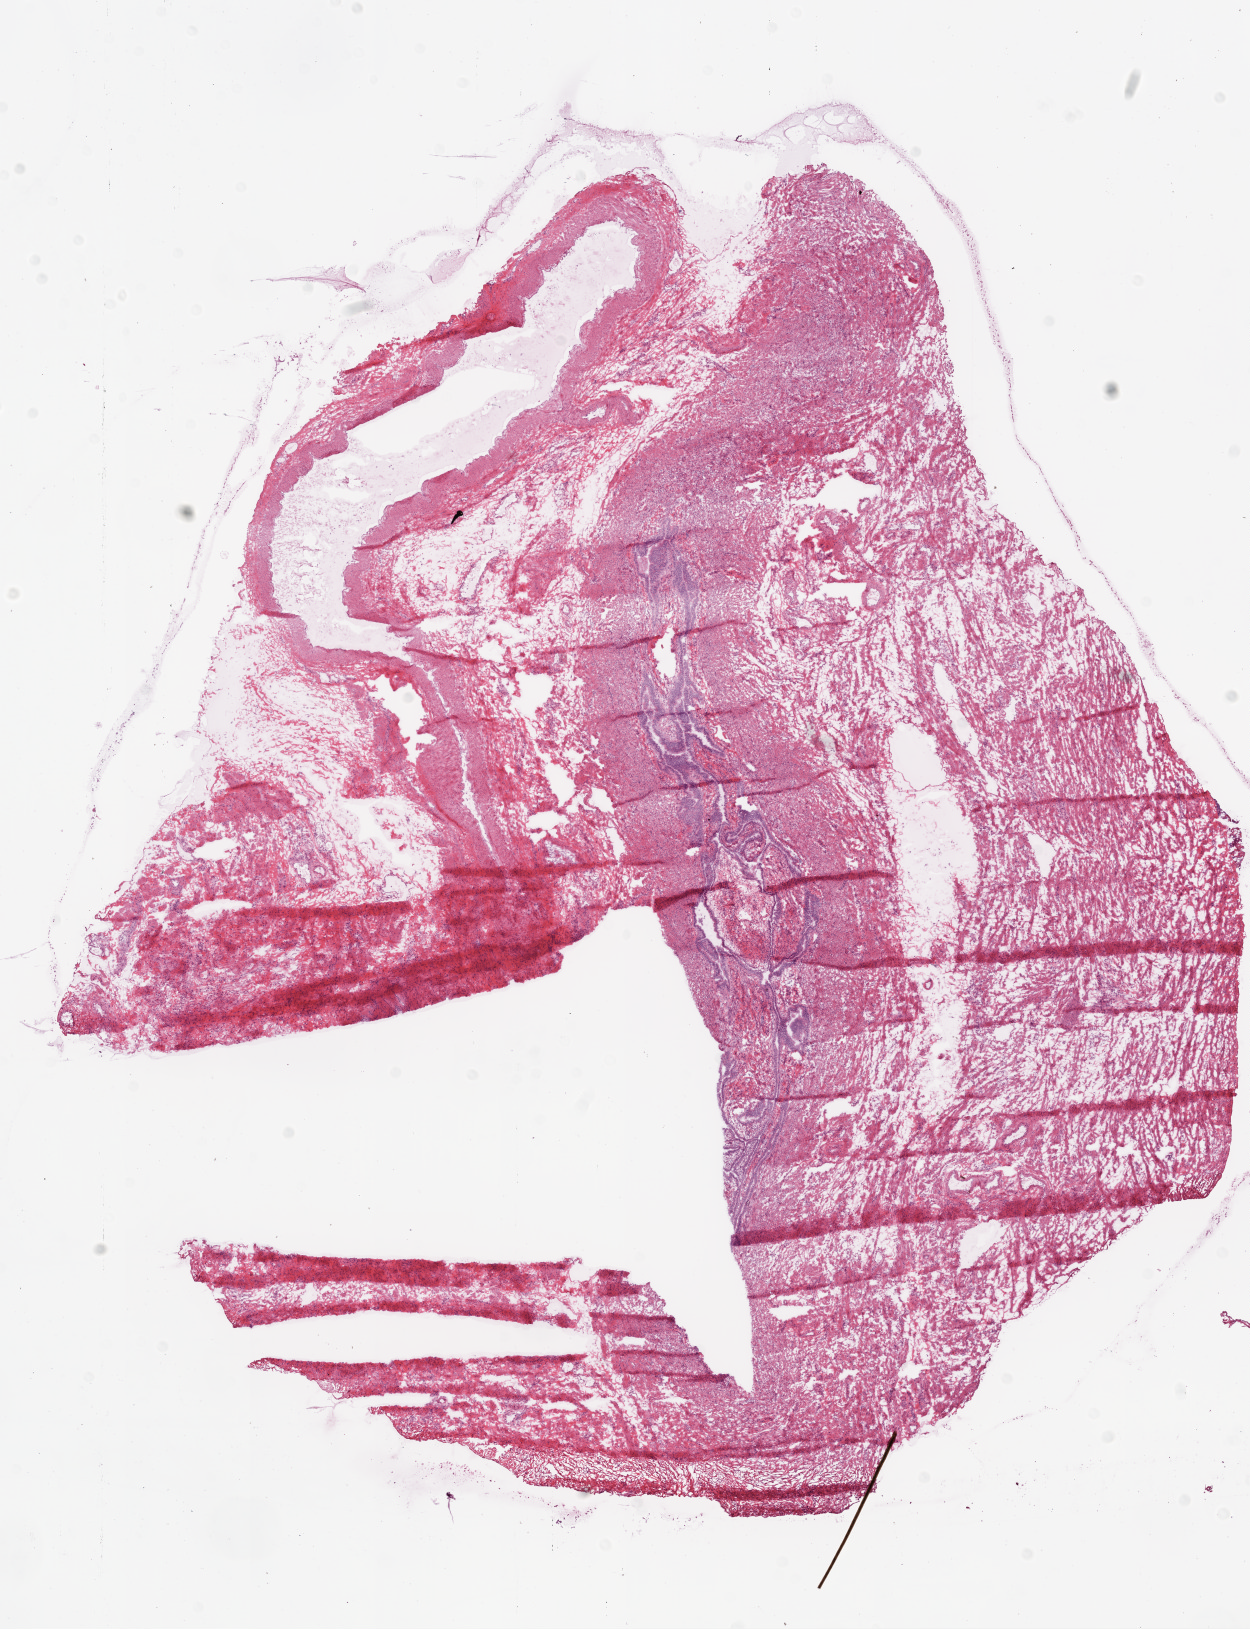
Digitized H&E tissue section (whole slide), whole scanned area (about 10.0 x 13.1 mm) shown as a low-resolution overview, frozen section, sample: solid tissue normal (non-tumour tissue), ovary. Female patient; age at initial diagnosis 40 years.
This section: solid tissue normal sample (biorepository sample class). Patient diagnosis: Serous cystadenocarcinoma, NOS.